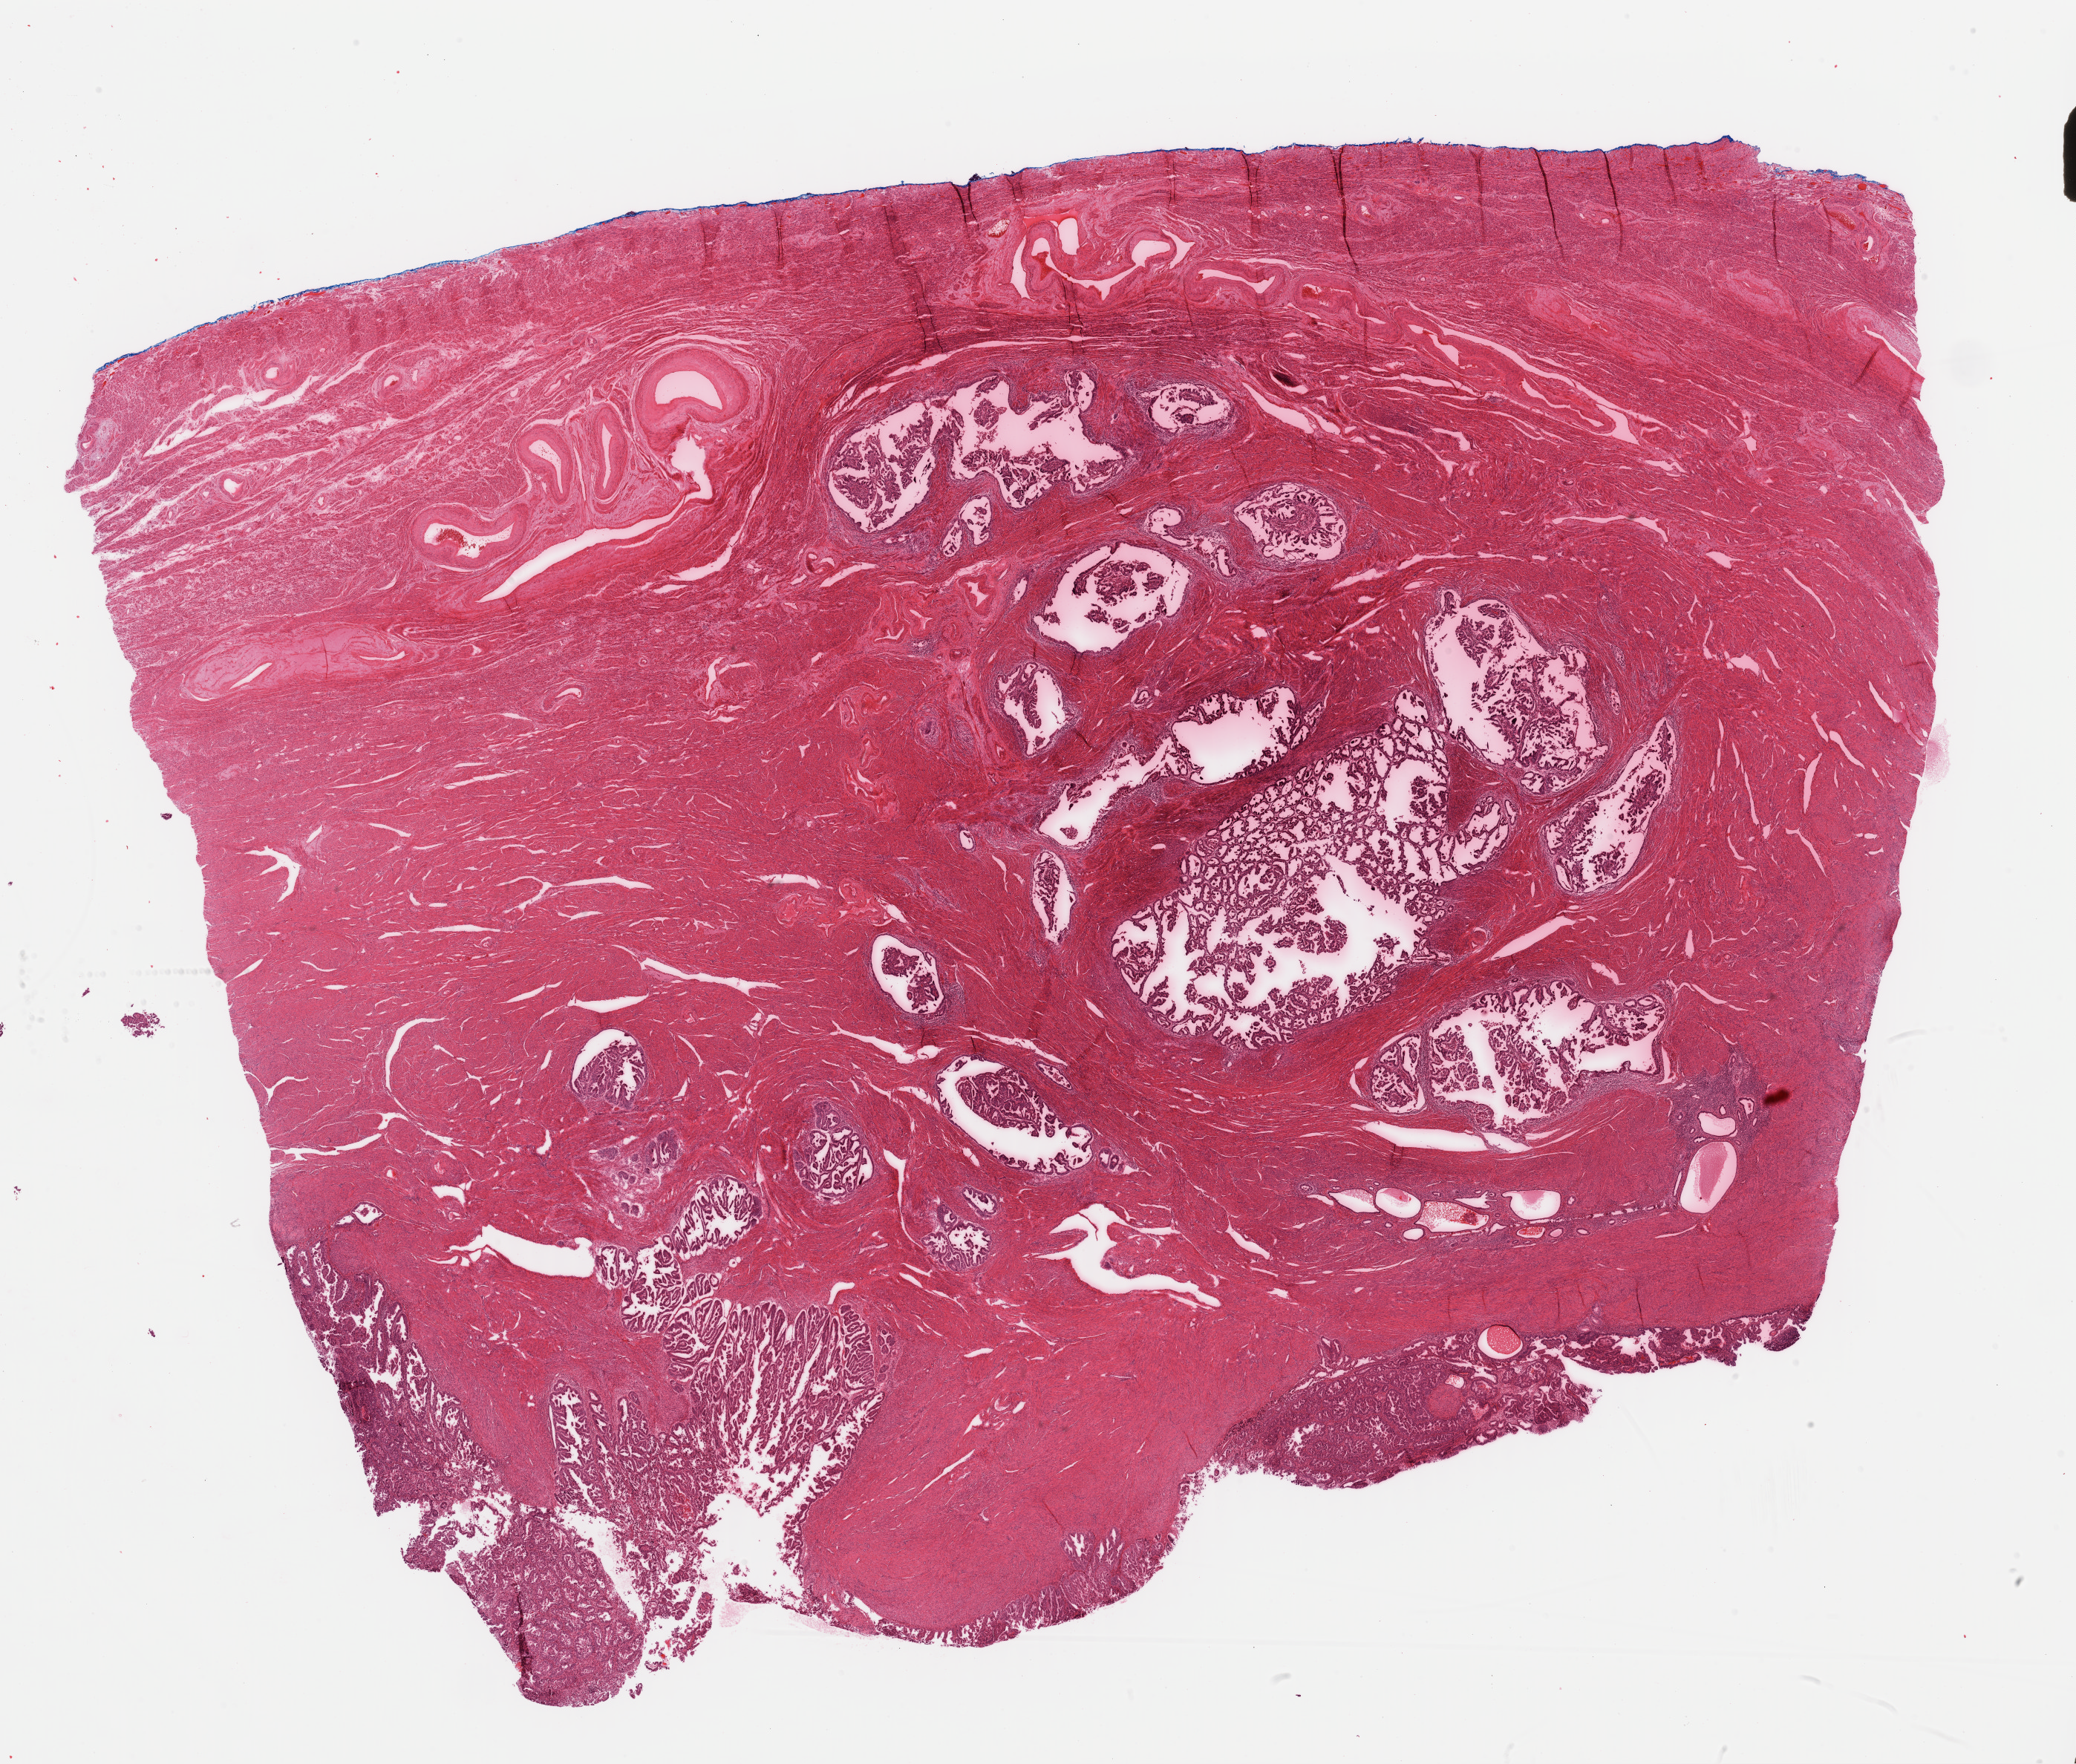
Whole-slide histology image, Hematoxylin and eosin (H&E) stained — low-resolution overview of the scanned area, about 22.1 x 18.8 mm, FFPE section, uterus, primary tumour sample. Female, age 79 years at initial diagnosis. Histologic grade: G3 (poorly differentiated).
- FIGO stage: IIIC
- diagnosis: Serous cystadenocarcinoma, NOS (endometrium)